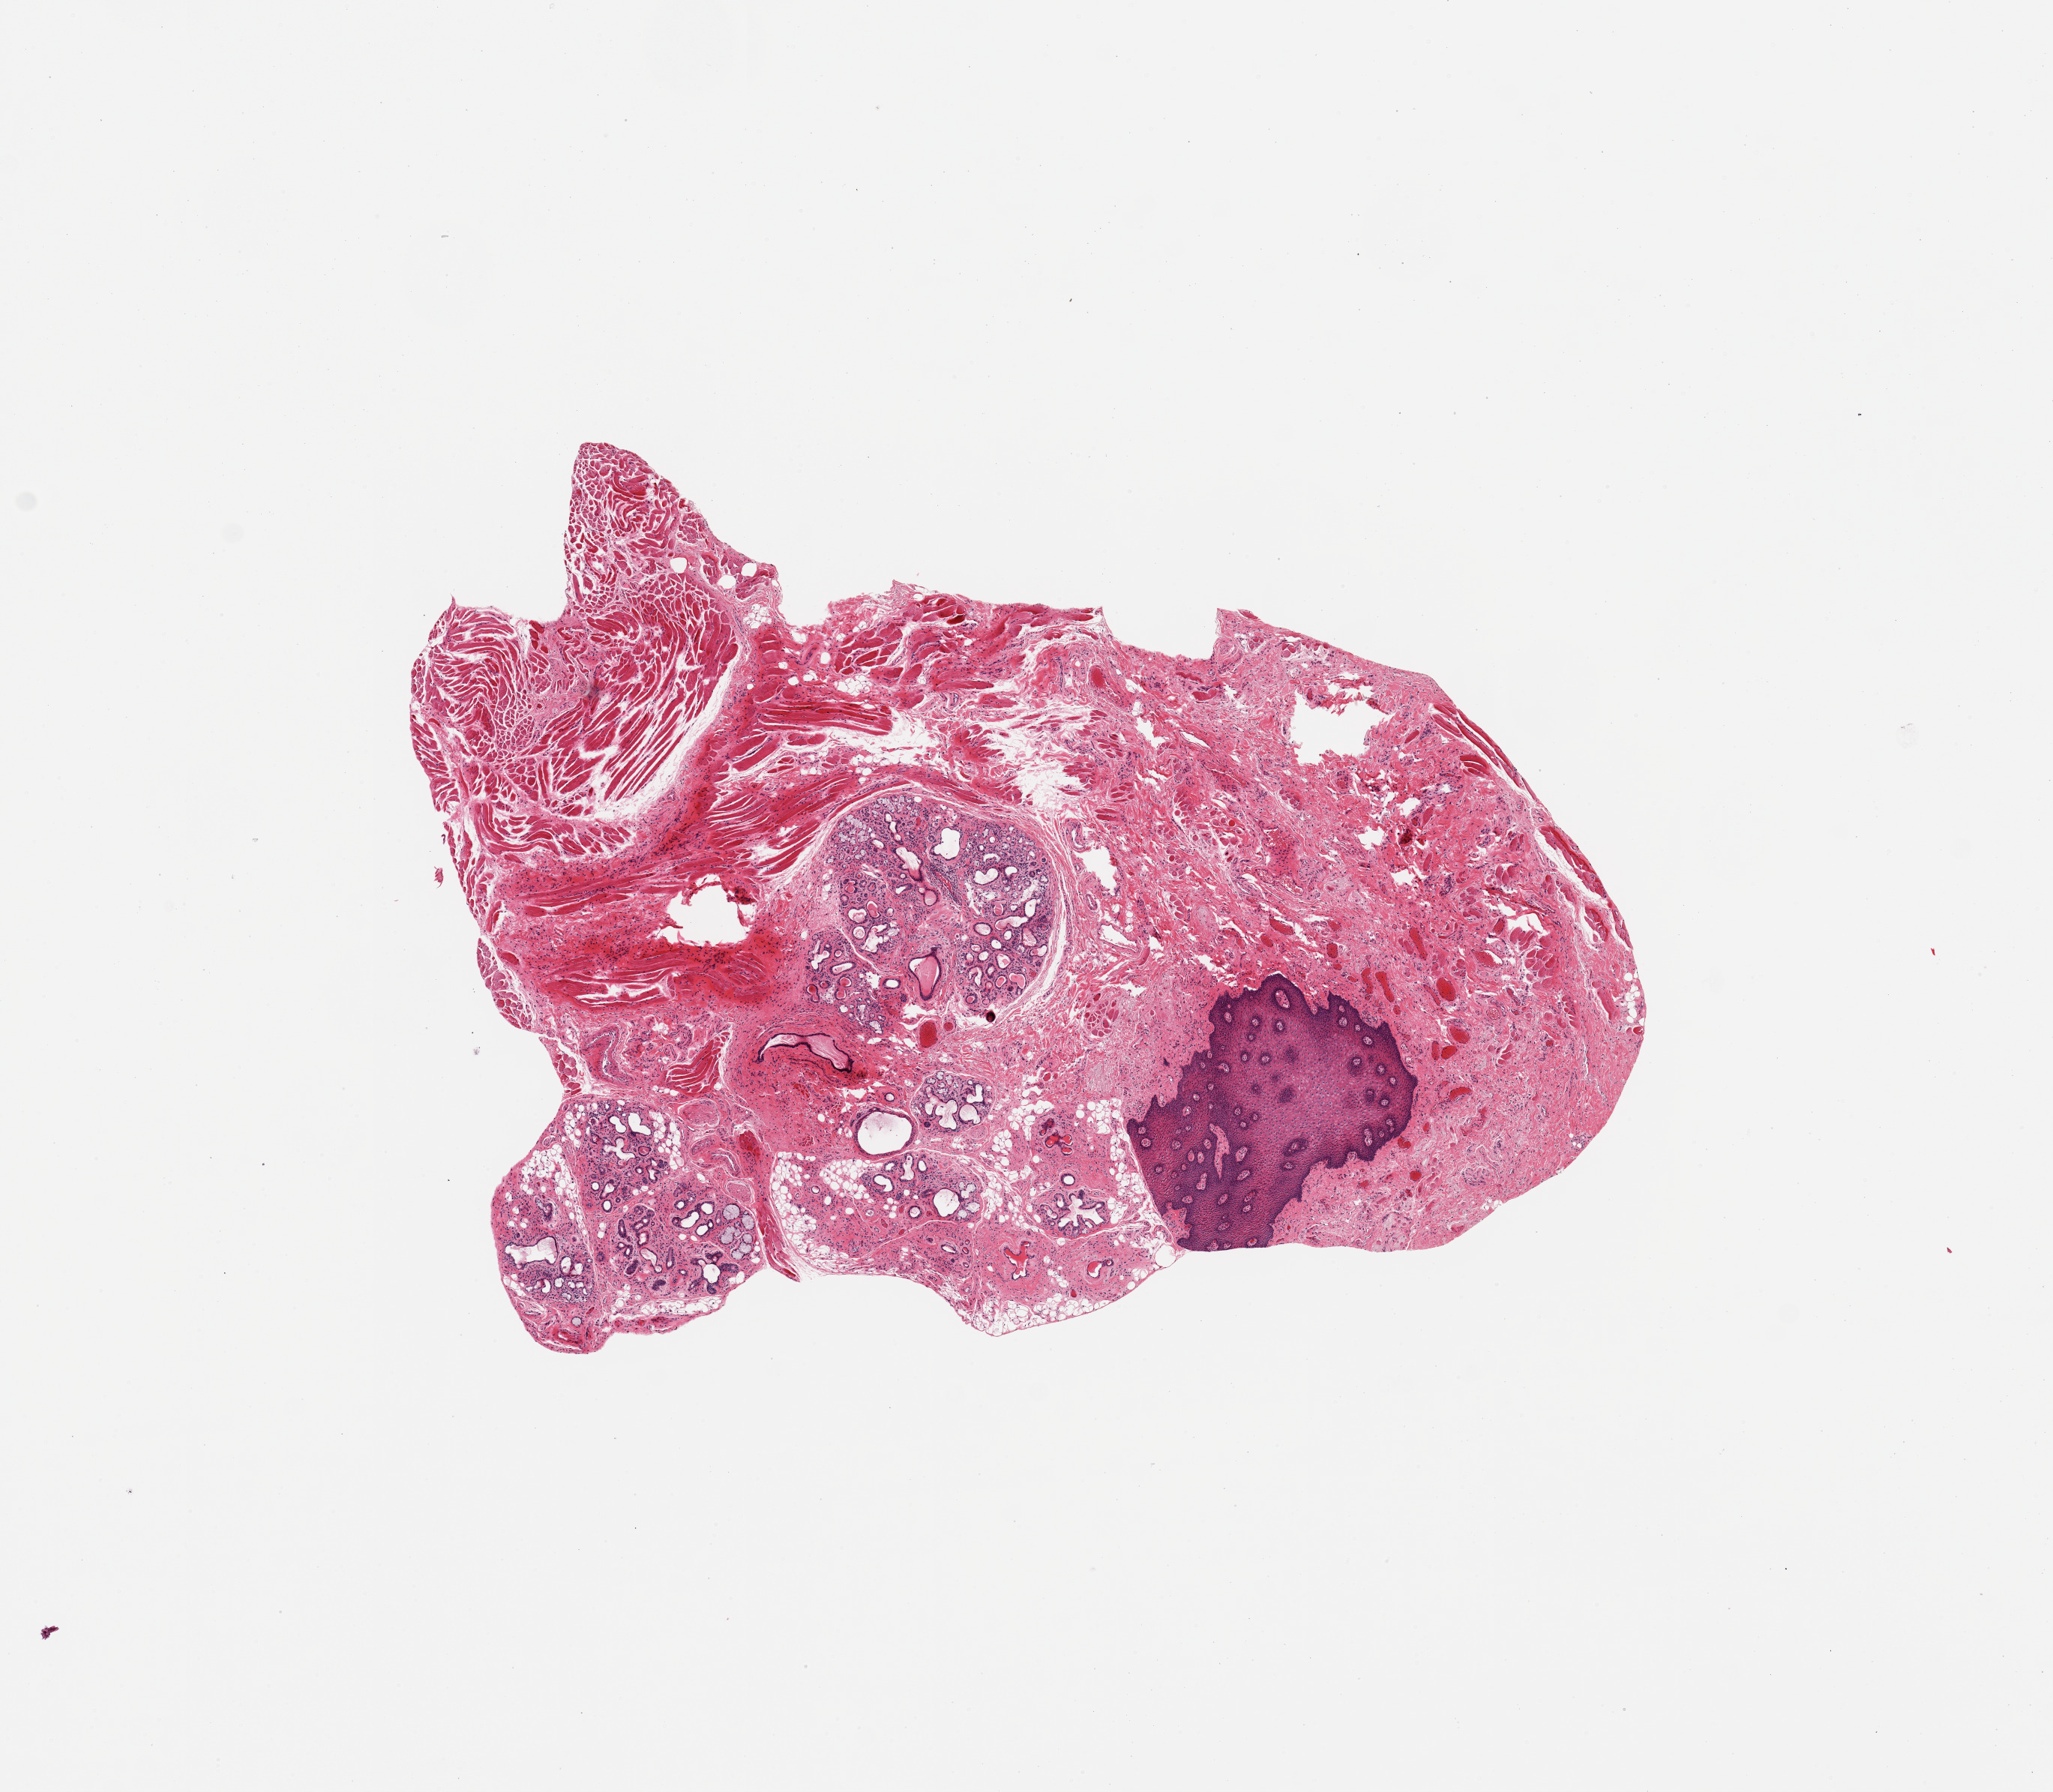
Whole-slide image, H&E stain, low-resolution overview of the scanned area, about 10.8 x 9.5 mm. PAXgene-fixed, paraffin-embedded tissue. Sampled site (target tissue): minor salivary gland. Donor tissue sample. Donor: male.
Pathologist's review note for this sample: 1 piece; salivary gland (~35%)surrounded by lip, stroma, and skeletal muscle representing (~65%).